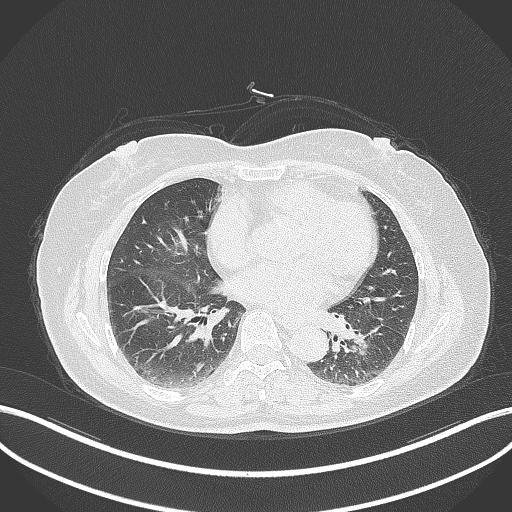
Chest CT, one axial slice; slice 165 of 311 in the series (ordered by position); 120 kVp; lung window (W 1500 / L -600 HU); 1 mm slice thickness; 512 × 512 image matrix, field of view 400 × 400 mm. Female patient, age 59 years. Case-level facts recorded for this patient, not image findings: clinical TNM (as recorded): T2a N0 M0; histopathological grade: G2-3.
Structures marked on this image (bounding box drawn by a radiologist):
- lung tumour (recorded histology: adenocarcinoma): bounding box (x1, y1, x2, y2) in pixels: (339, 325, 383, 360)